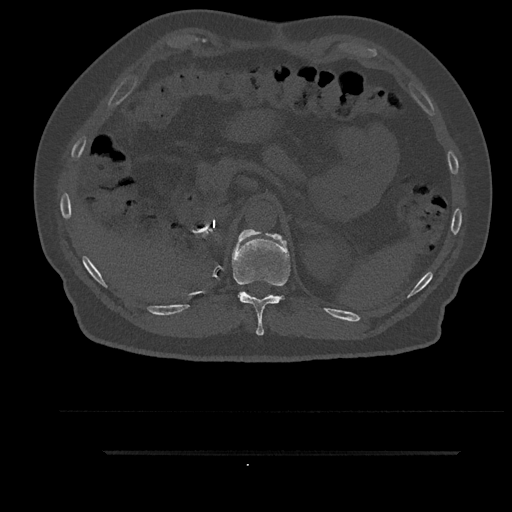
CT including the spine, one axial slice. Position 292 of 797 along the scan axis. Reconstruction kernel Br40s/3. Bone window (W 1800 / L 400 HU). 0.5 mm slice thickness. 512 × 512 image matrix, field of view 432 × 432 mm. Male patient, age 63 years. From the clinical record (not read from this slice): primary cancer: renal; vertebrae with lytic lesions (as recorded): T8.
Outlined on this slice (semi-automatically segmented with operator editing):
- T11 vertebra: bounding box (x1, y1, x2, y2) in pixels: (232, 229, 291, 336)
- T12 vertebra: (238, 229, 256, 241)